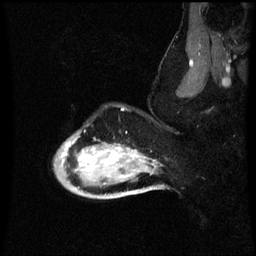
Breast MRI (dynamic contrast-enhanced), one sagittal slice; slice 50 of 60 in the series (ordered by position); dynamic contrast-enhanced series, image 2 of 3 at this slice position (ordered by acquisition); 1.5 T; TE 4.2 ms, TR 8.9 ms; 256 × 256 image matrix, field of view 200 × 200 mm. Patient: female, 49 years. From the clinical record (not read from this slice): setting: breast cancer imaged before/during neoadjuvant chemotherapy; receptor status: HR-positive, HER2-negative.
Structures marked on this image (semi-automatically segmented with operator editing):
- analysis volume of interest (the breast-tissue region the enhancement analysis was run in; not a lesion): bounding box (x1, y1, x2, y2) in pixels: (54, 130, 159, 199)
- tumour enhancement mask (voxels above the 70 % enhancement threshold inside the analysis volume of interest): (64, 142, 145, 171)